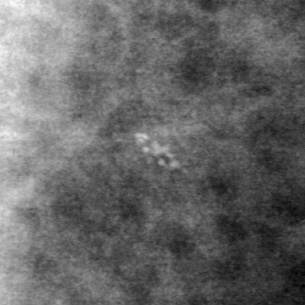
Region of interest cut from a scanned film mammogram (one marked finding), right breast, MLO view.
Marked abnormality: calcifications, morphology pleomorphic, distribution clustered; BI-RADS assessment category 4; pathology result (as recorded, not read from the image): benign.